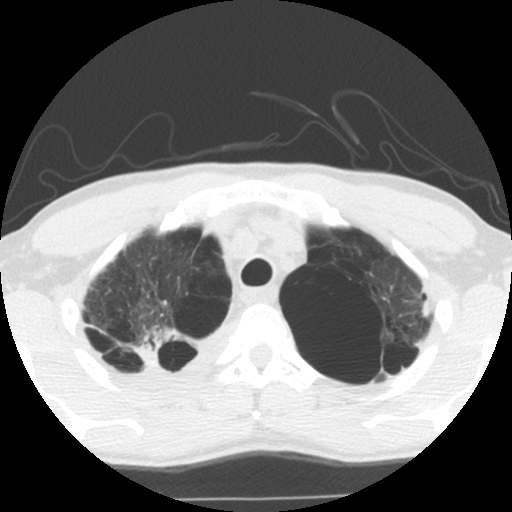
Low-dose screening chest CT, one axial slice; position 97 of 119 along the scan axis; reconstruction kernel STANDARD; lung window (W 1500 / L -600 HU); 2.5 mm slice thickness; 512 × 512 image matrix.
Structures marked on this image (outlined manually by an expert reader):
- lesion 1 (tumor, upper lobe of right lung): bounding box [x1, y1, x2, y2] px = [136, 323, 181, 360]